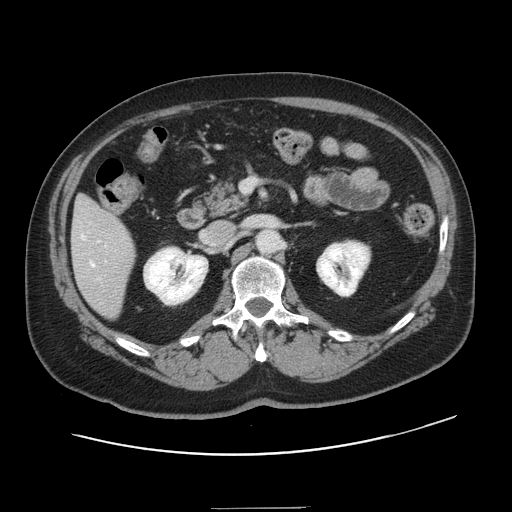
Contrast-enhanced abdominal CT, one axial slice. Slice 63 of 143 in the series (ordered by position). 120 kVp. Intravenous contrast given. Soft-tissue window (W 400 / L 40 HU). 2.5 mm slice thickness. 512 × 512 image matrix, field of view 402 × 402 mm. Male patient, age 62 years. From the clinical record (not read from this slice): diagnosis: colorectal cancer liver metastases, imaged before liver resection; multiple liver metastases: yes; largest metastasis: 2.7 cm.
Outlined on this slice (manually delineated by an expert):
- hepatic veins: bounding box [x1, y1, x2, y2] px = [81, 235, 95, 267]
- liver: [73, 198, 135, 318]
- planned liver remnant (the part of the liver to remain after resection): [77, 197, 93, 209]
- portal vein (with intrahepatic branches): [98, 241, 106, 262]